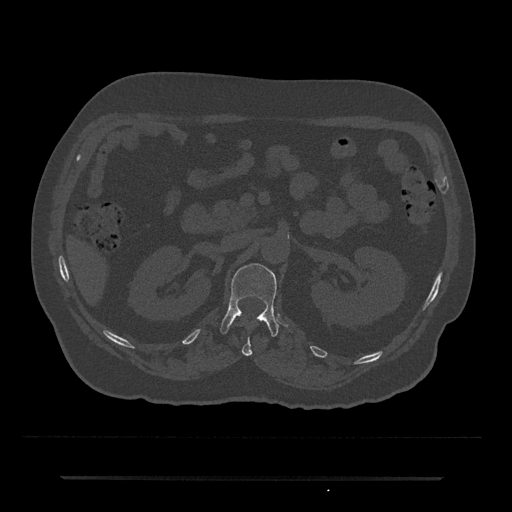
CT including the spine, one axial slice. Slice 85 of 797 in the series (ordered by position). 120 kVp. Bone window (W 1800 / L 400 HU). 0.5 mm slice thickness. 512 × 512 image matrix, field of view 437 × 437 mm. Male patient, age 69 years. From the clinical record (not read from this slice): primary cancer: prostate.
Structures marked on this image (semi-automatic segmentation, software-assisted and operator-edited):
- L1 vertebra: bounding box (x1, y1, x2, y2) in pixels: (220, 263, 279, 337)
- T12 vertebra: (242, 323, 252, 356)